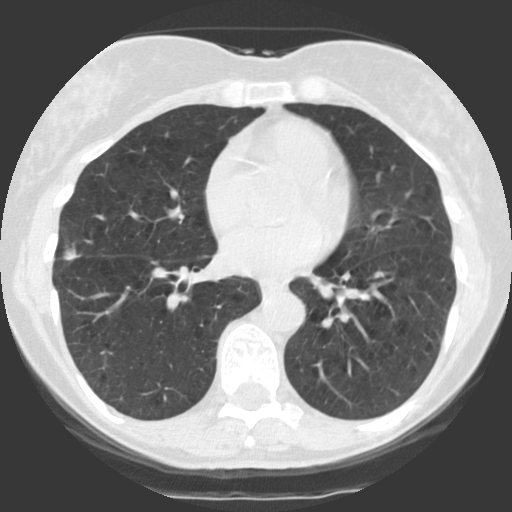
Low-dose screening chest CT, one axial slice. Slice 55 of 123 in the series (ordered by position). Reconstruction kernel STANDARD. 140 kVp. Lung window (W 1500 / L -600 HU). 2.5 mm slice thickness. 512 × 512 image matrix, field of view 290 × 290 mm.
Annotated regions visible in this slice (expert manual segmentation):
- lesion 1 (tumor, middle lobe of right lung): box from (x=64, y=249) to (x=81, y=261) px